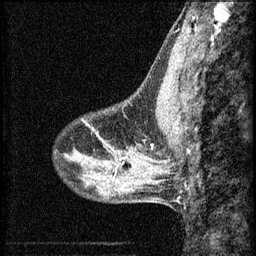
Breast MRI (dynamic contrast-enhanced), one sagittal slice; position 19 of 60 along the scan axis; 3 images stored at this slice position (order not interpretable as contrast timing); 1.5 T; TE 4.2 ms, TR 8.2 ms; 2 mm slice thickness; 256 × 256 image matrix, field of view 180 × 180 mm. Patient: female, 40 years.
Outlined on this slice (semi-automatically segmented with operator editing):
- analysis volume of interest (the breast-tissue region the enhancement analysis was run in; not a lesion): bounding box (x1, y1, x2, y2) in pixels: (104, 116, 159, 165)
- tumour enhancement mask (voxels above the 70 % enhancement threshold inside the analysis volume of interest): (120, 160, 125, 165)